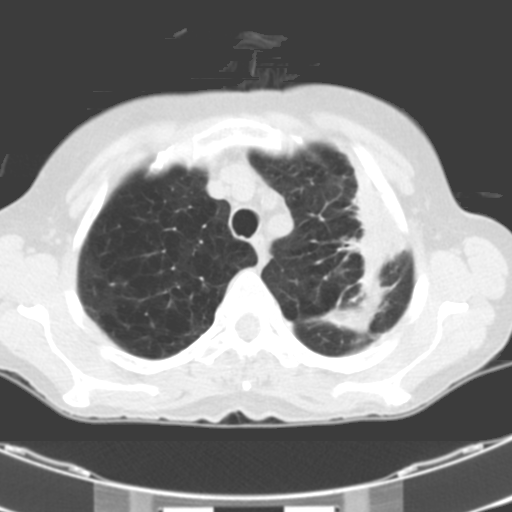
Low-dose screening chest CT, one axial slice. Slice 85 of 106 in the series (ordered by position). 120 kVp. One of 2 acquisitions stored at this slice position. Lung window (W 1500 / L -600 HU). 3.2 mm slice thickness. 512 × 512 image matrix.
Structures marked on this image (outlined manually by an expert reader):
- lesion 1 (tumor): bounding box <323,308,371,333> (left, top, right, bottom; pixels)